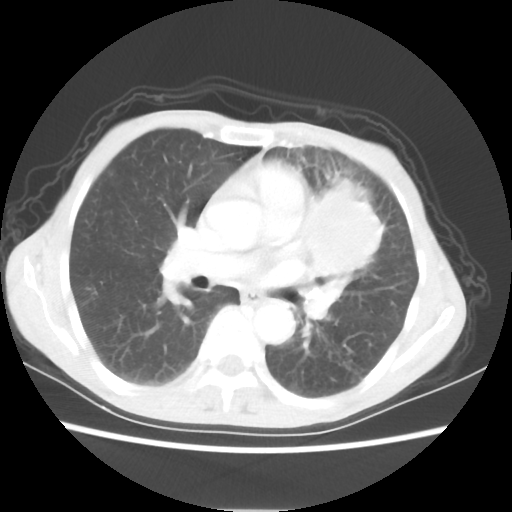
Chest CT, one axial slice; slice 33 of 56 in the series (ordered by position); lung window (W 1500 / L -600 HU); 5 mm slice thickness; 512 × 512 image matrix, field of view 331 × 331 mm. Patient: female, 60 years. From the clinical record (not read from this slice): clinical TNM (as recorded): T4 N1 M0.
Annotated regions visible in this slice (bounding box drawn by a radiologist):
- lung tumour (recorded histology: adenocarcinoma): bounding box [x1, y1, x2, y2] px = [295, 165, 395, 292]